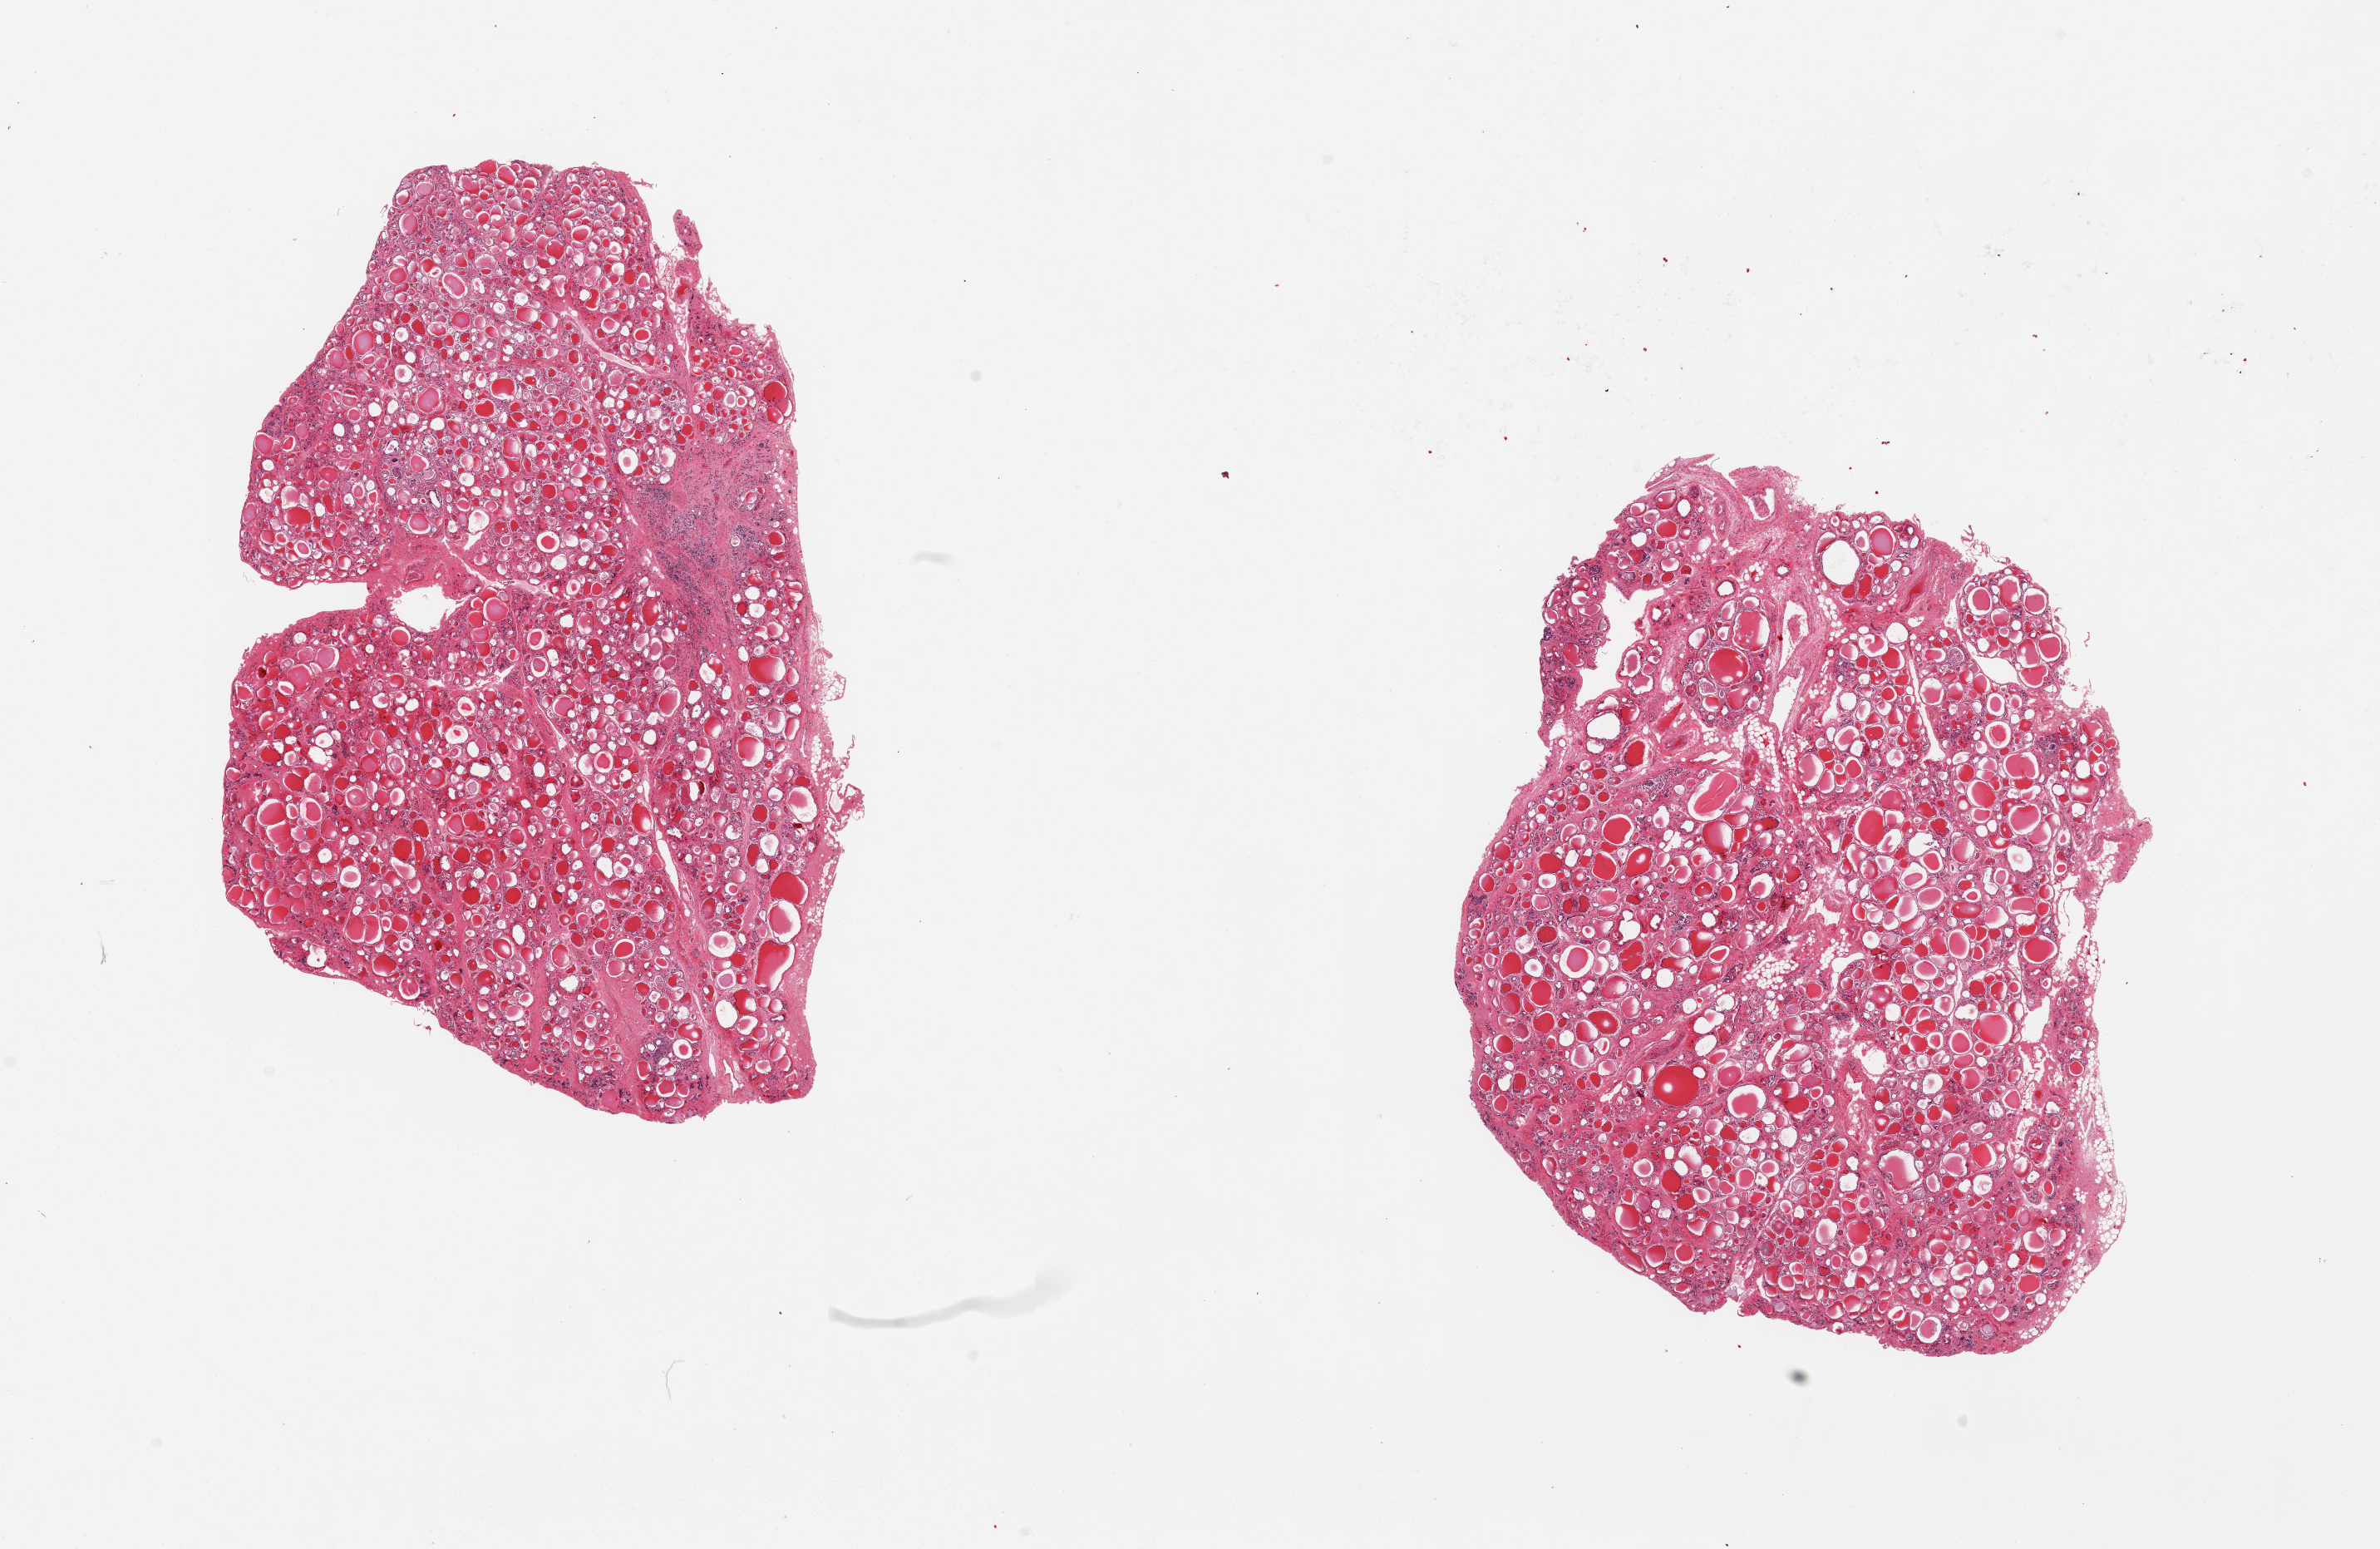
Digitized H&E-stained section — shown as a low-resolution overview of the whole scanned area (about 22.6 x 14.7 mm, slide scanned at 20x), PAXgene-fixed paraffin-embedded (PFPE) section, target tissue: thyroid, donor tissue sample. Female donor.
Pathologist's review note for this sample: 2 pieces; 1.5 mm focus of atrophy & fibrosis.